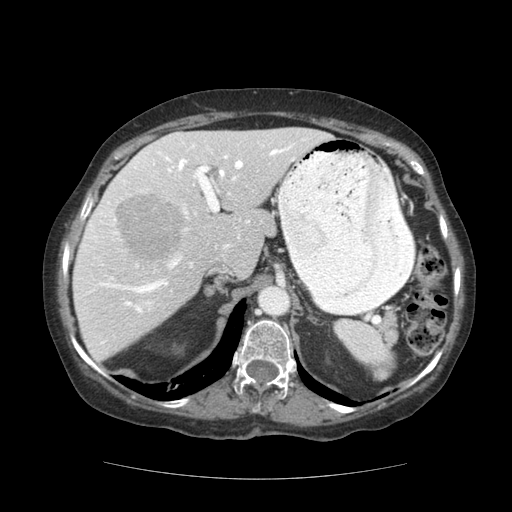
Contrast-enhanced abdominal CT (liver protocol), one axial slice; position 79 of 111 along the scan axis; 140 kVp; soft-tissue window (W 400 / L 40 HU); 512 × 512 image matrix, field of view 360 × 360 mm. From the clinical record (not read from this slice): diagnosis: hepatocellular carcinoma (patient treated with transarterial chemoembolisation; whether this scan precedes or follows treatment is not stated here); TNM stage (as recorded): Stage-I; Child-Pugh class: A.
Outlined on this slice (semi-automatic segmentation, software-assisted and operator-edited):
- liver parenchyma outside the tumour (the mass and vessels are separate outlines, so this box may not span the whole liver): bounding box [x1, y1, x2, y2] px = [72, 128, 331, 360]
- mass: [116, 193, 183, 261]
- liver vessels: [83, 139, 306, 344]